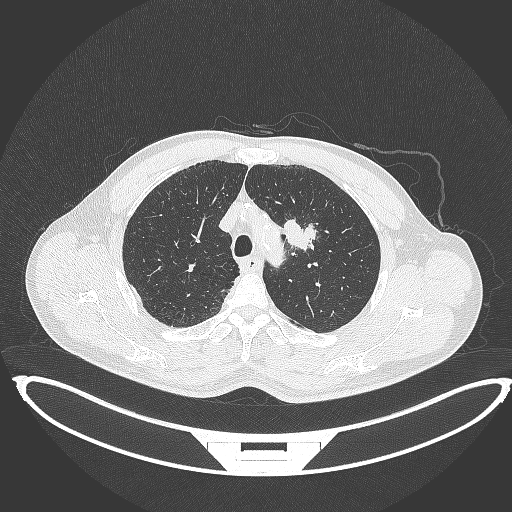
Chest CT, one axial slice. Position 338 of 395 along the scan axis. Reconstruction kernel B70f. Lung window (W 1500 / L -600 HU). 512 × 512 image matrix, field of view 457 × 457 mm. Male patient, age 60 years. Case-level facts recorded for this patient, not image findings: clinical TNM (as recorded): T2a N0 M0.
Structures marked on this image (bounding box drawn by a radiologist):
- lung tumour (recorded histology: squamous cell carcinoma): bounding box [x1, y1, x2, y2] px = [280, 214, 317, 256]